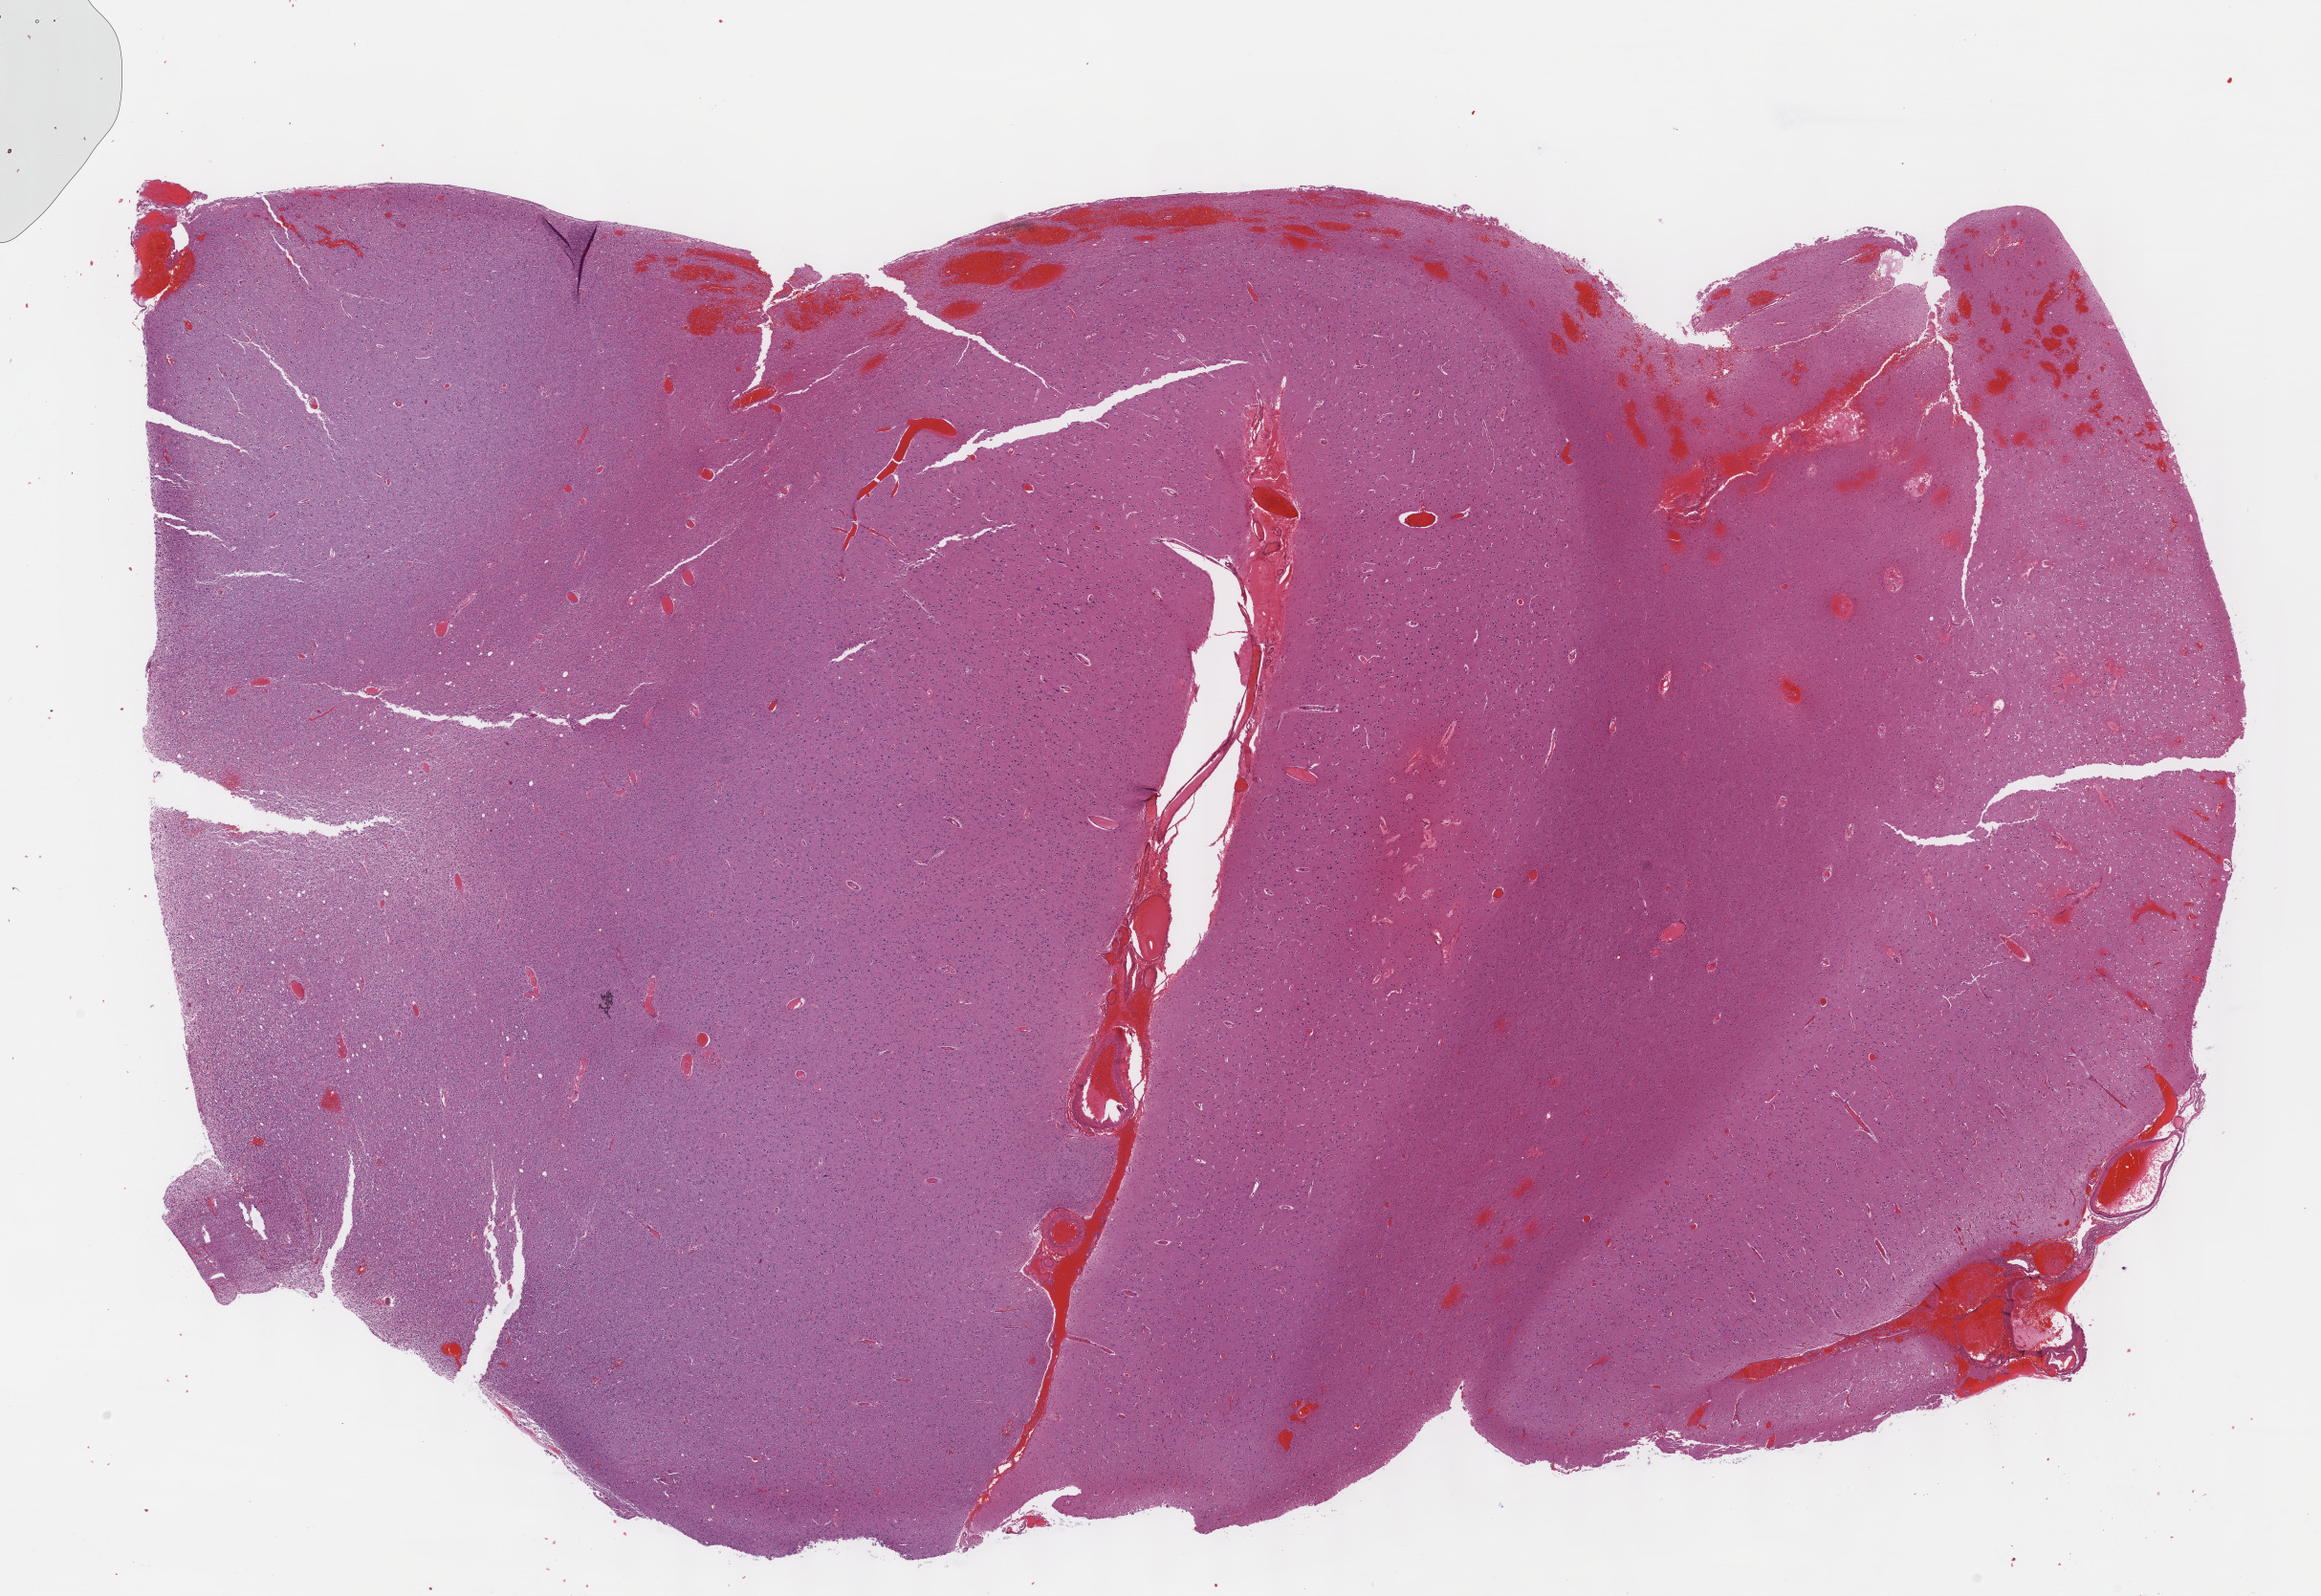
Whole-slide histology image, H&E-stained — a low-resolution overview of the entire scanned area, about 19.6 x 13.5 mm (from a 40x scan); formalin-fixed paraffin-embedded (FFPE) diagnostic section; primary tumour sample from the brain. Patient: female, age at initial diagnosis 20 years. Histologic grade: G2 (moderately differentiated).
- histologic diagnosis: Oligodendroglioma, NOS (cerebrum)
- laterality: left